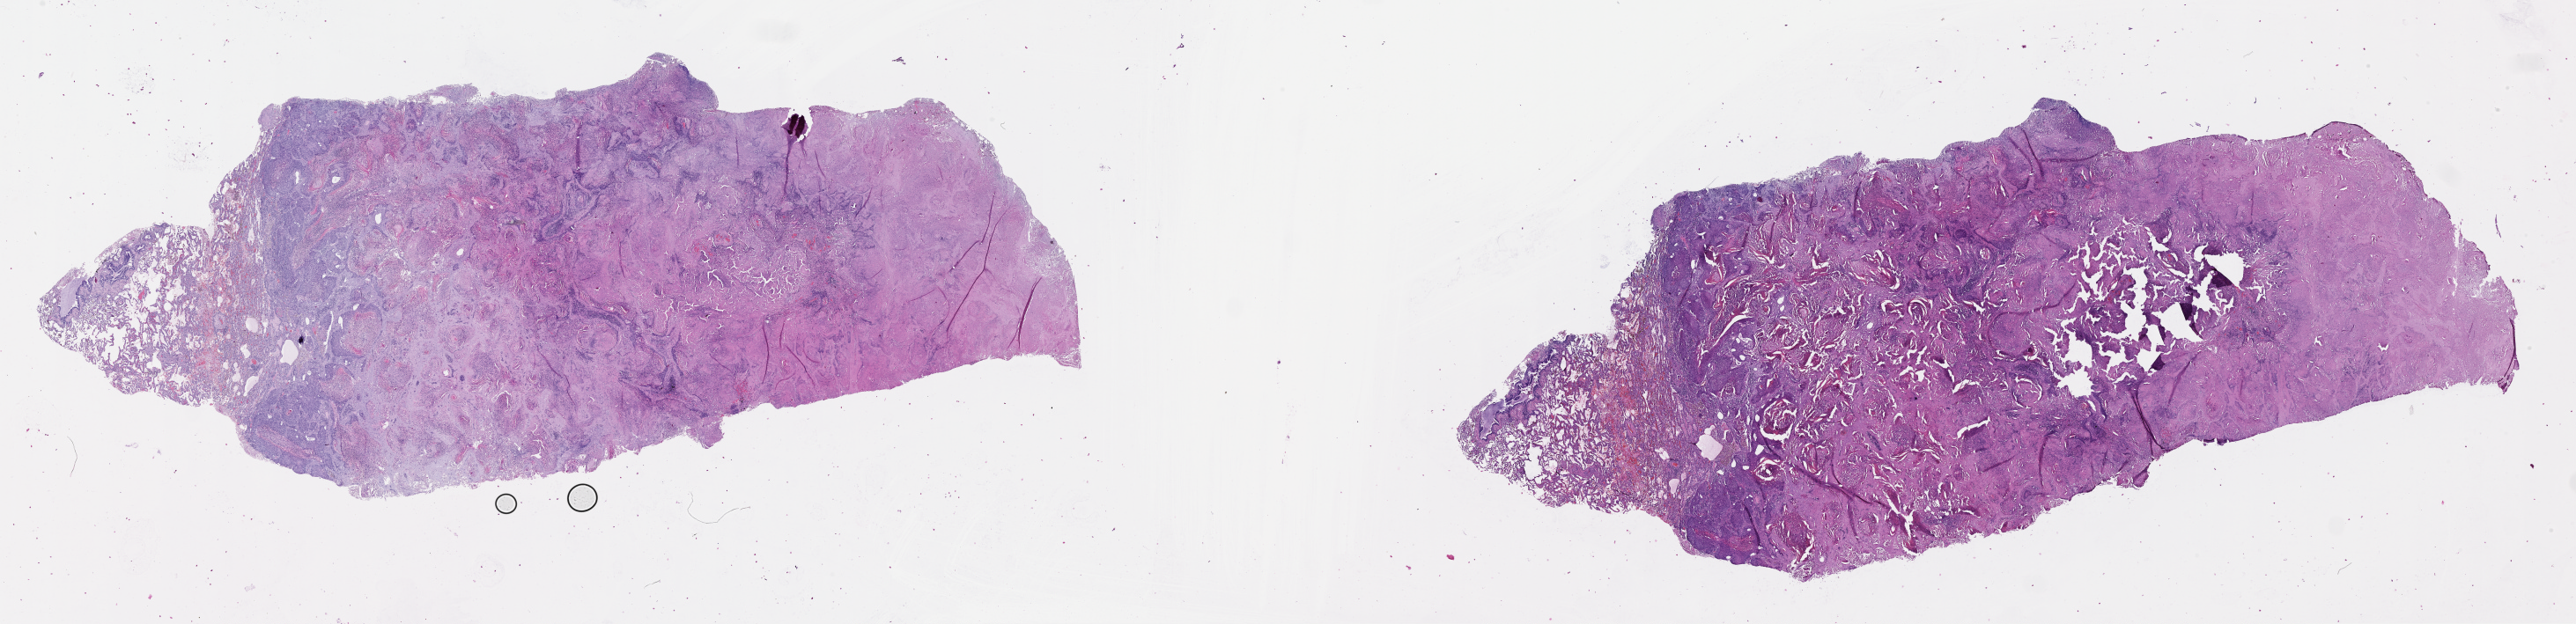
H&E whole-slide image — a low-resolution overview of the entire scanned area, about 47.1 x 11.4 mm. Lung, tumour tissue. Patient: male, age 49 years.
Patient diagnosis (cohort enrolment): squamous cell carcinoma (lung).